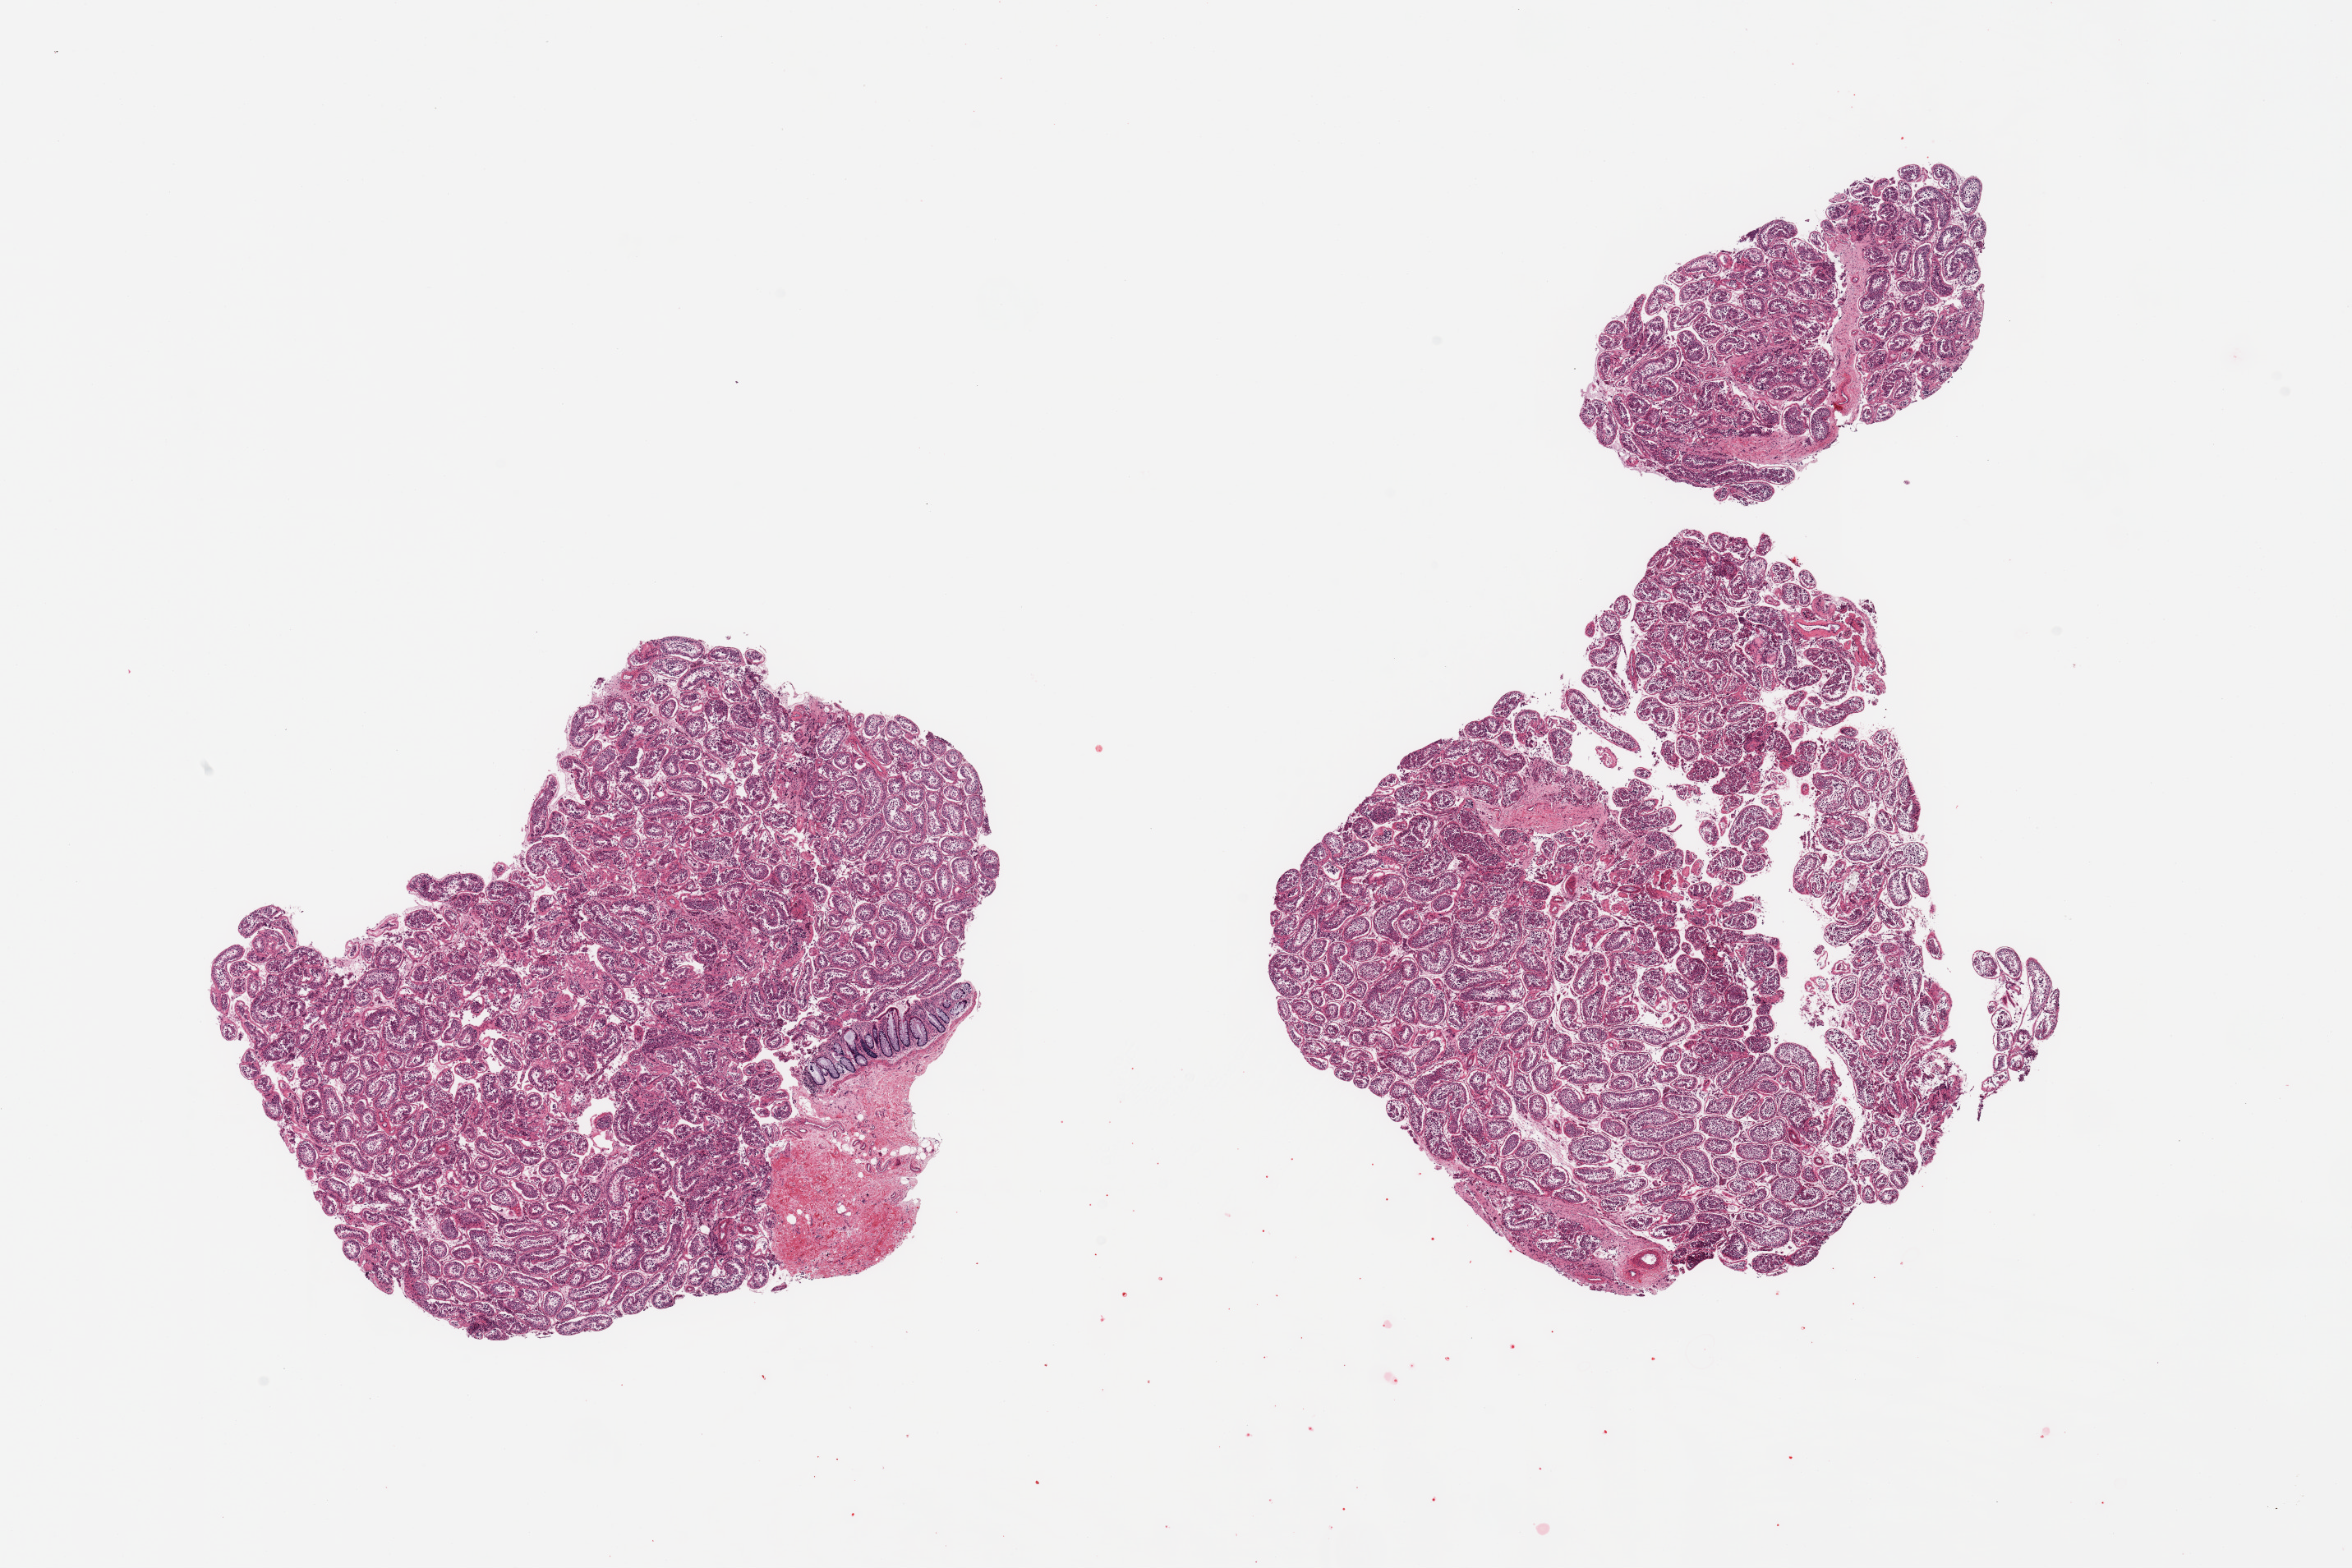
Haematoxylin and eosin whole-slide image, brightfield — a low-resolution overview of the entire scanned area, about 22.6 x 15.1 mm (from a 20x scan). PAXgene-fixed paraffin-embedded (PFPE) section. Section of testis (target tissue). Donor tissue sample. Male donor.
Review note (as recorded): 3 pieces; spermatogenesis with reduced number of mature sperm; colon mucosa/submucosa (4 sq mm) attached to 1 piece.